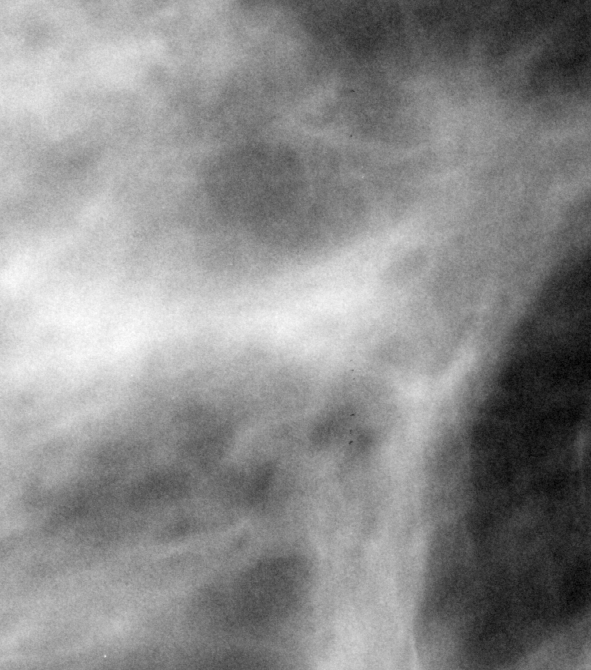
Cropped region of a digitized screen-film mammogram centred on a radiologist-marked abnormality, right breast, MLO view.
Mass, shape architectural distortion, margins ill defined; BI-RADS assessment category 5; subtlety rating 5 on a 1 (subtle) to 5 (obvious) scale; pathology result (as recorded, not read from the image): malignant.